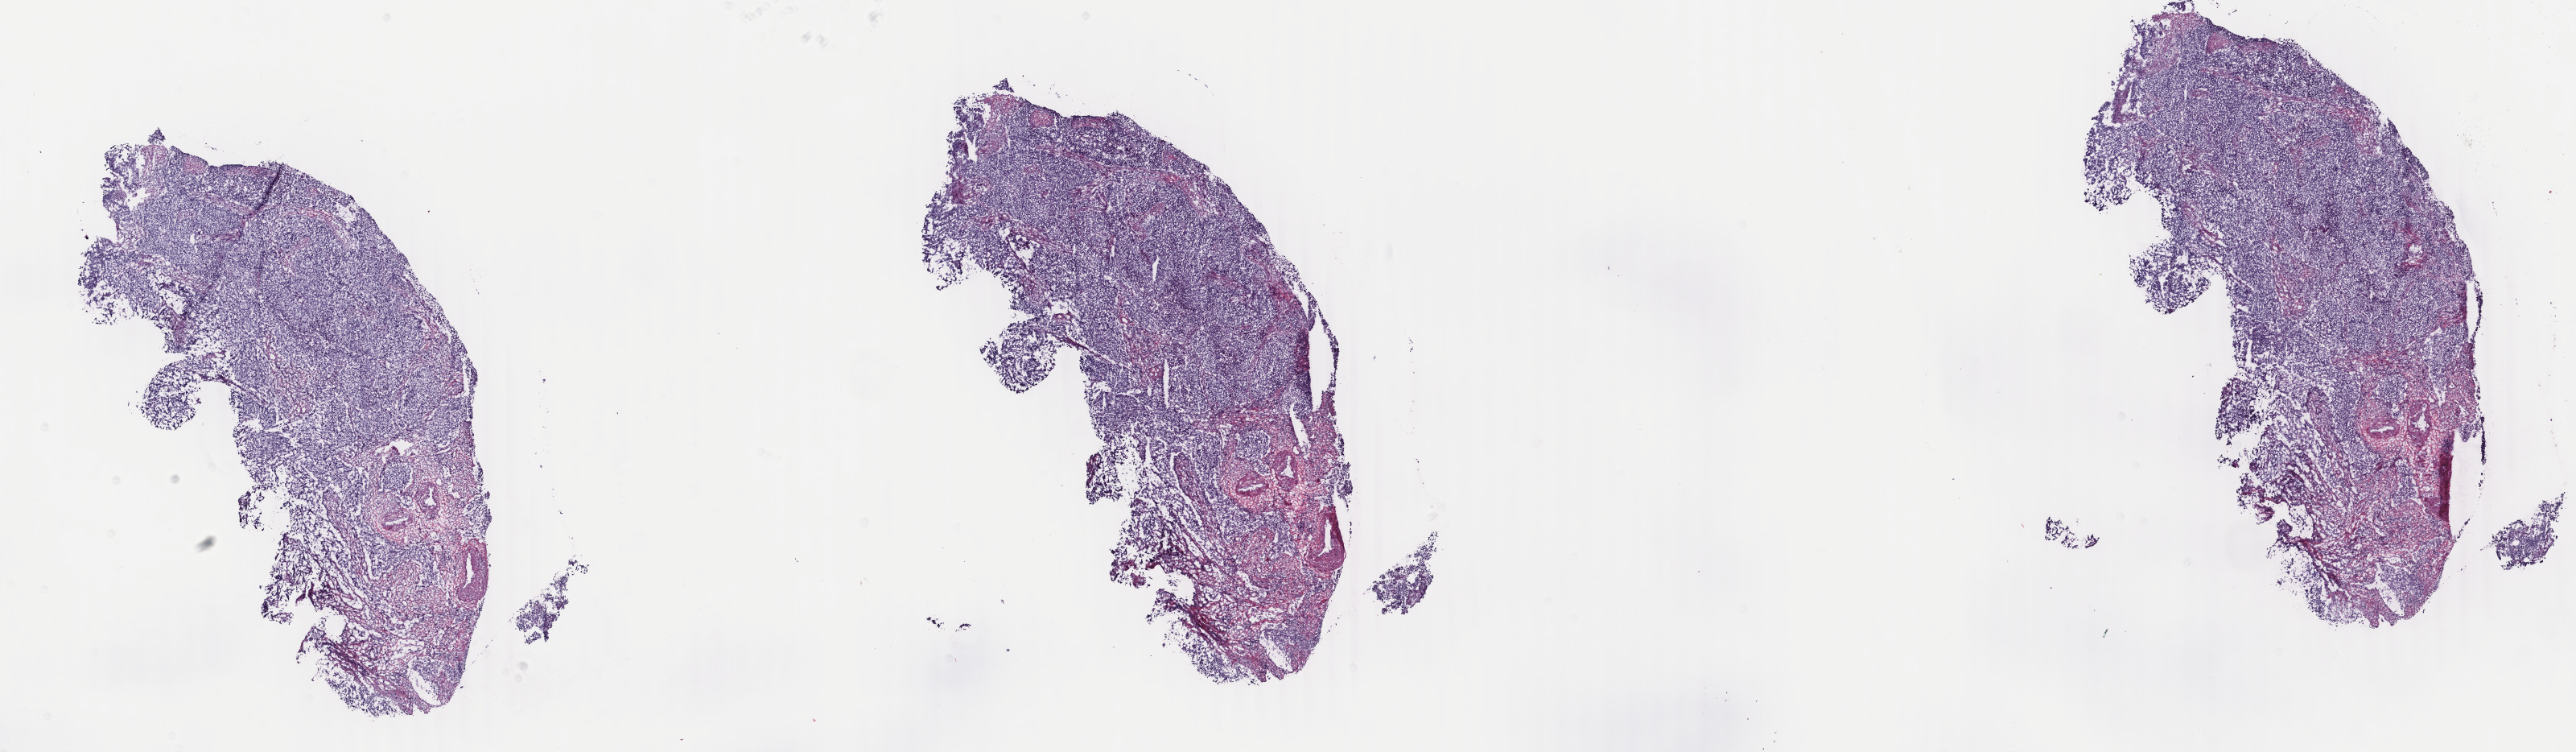
H&E-stained whole-slide image — a low-resolution overview of the entire scanned area, about 25.5 x 7.4 mm (acquisition: 40x scan), frozen section, uterus, primary tumour sample. Female patient; age at initial diagnosis 67 years. Histologic grade: G3 (poorly differentiated). Composition of this section per pathologist review: tumour cells 80%, tumour nuclei 75%, normal cells 0%, stromal cells 20%, necrosis 0%. Infiltration values recorded for this section: lymphocyte infiltration 0%, monocyte infiltration 0%, neutrophil infiltration 0%.
* pathologic diagnosis: Endometrioid adenocarcinoma, NOS (endometrium)
* FIGO stage: IIIC2